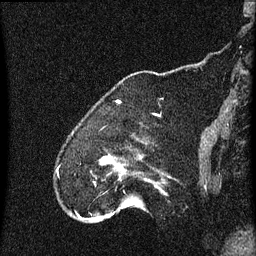
Breast MRI (dynamic contrast-enhanced), one sagittal slice. Position 10 of 60 along the scan axis. Dynamic contrast-enhanced series, image 2 of 4 at this slice position (ordered by acquisition). 1.5 T. TE 4.2 ms, TR 8 ms. 2 mm slice thickness. 256 × 256 image matrix, field of view 180 × 180 mm. Patient: female, 52 years.
Annotated regions visible in this slice (semi-automatically segmented with operator editing):
- analysis volume of interest (the breast-tissue region the enhancement analysis was run in; not a lesion): bounding box <73,152,164,219> (left, top, right, bottom; pixels)
- tumour enhancement mask (voxels above the 70 % enhancement threshold inside the analysis volume of interest): <104,158,117,165>